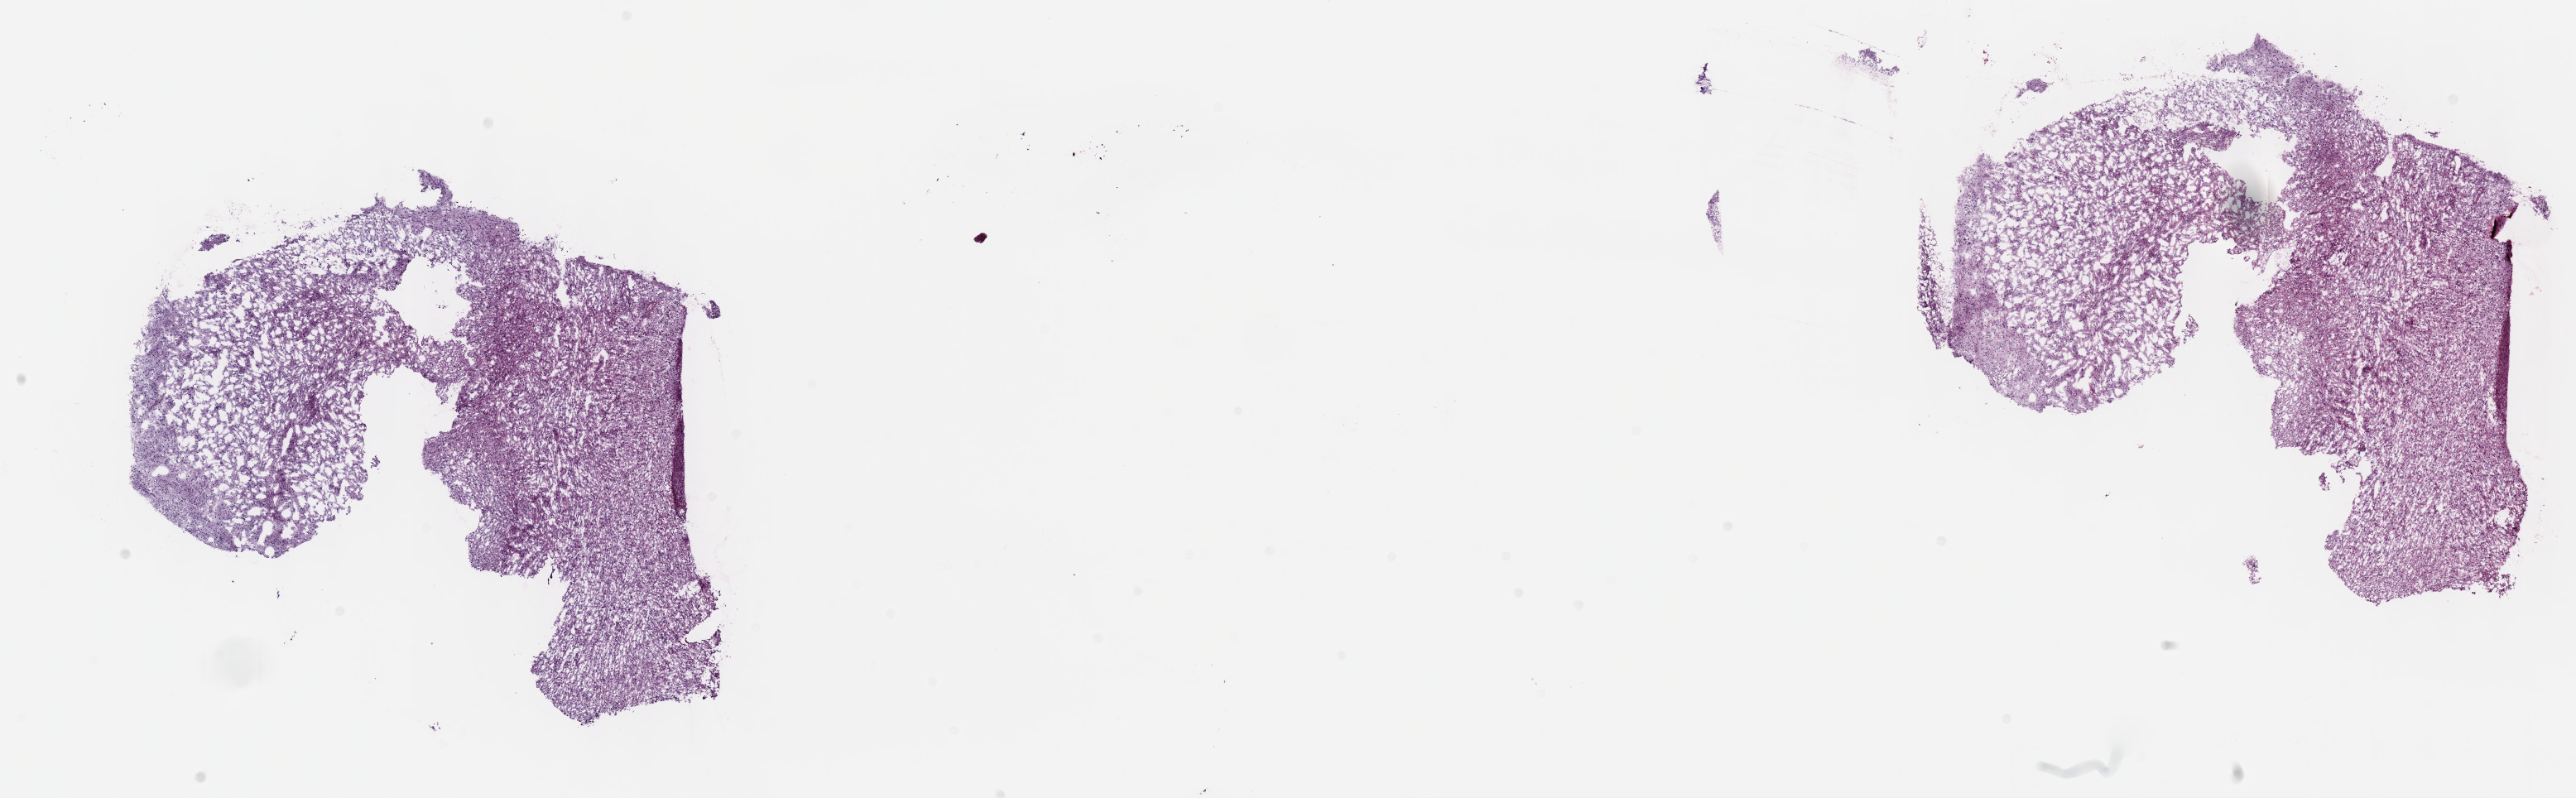
Whole-slide histology image, Hematoxylin and eosin (H&E) stained, a low-resolution overview of the entire scanned area, about 25.2 x 7.8 mm, frozen section from the top of the tissue portion, brain, primary tumour sample. Male patient; age at initial diagnosis 34 years. Histologic grade: G3 (poorly differentiated). Composition of this section per pathologist review: tumour cells 50%, tumour nuclei 90%, normal cells 5%, stromal cells 45%, necrosis 0%. Infiltration values recorded for this section: lymphocyte infiltration 0%, monocyte infiltration 0%, neutrophil infiltration 0%.
Laterality: left. Histologic diagnosis: Astrocytoma, anaplastic (cerebrum).